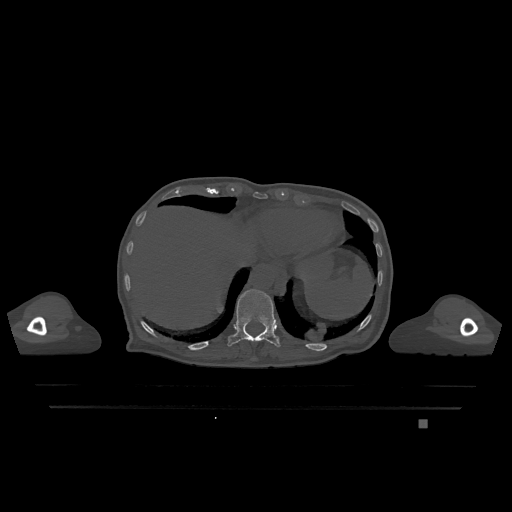
CT including the spine, one axial slice; slice 594 of 1317 in the series (ordered by position); bone window (W 1800 / L 400 HU); 0.5 mm slice thickness; 512 × 512 image matrix, field of view 500 × 500 mm. Patient: female, 74 years. From the clinical record (not read from this slice): primary cancer: lung; vertebrae with lytic lesions (as recorded): T1, T4, T5, T6, L4, L5.
Annotated regions visible in this slice (semi-automatic segmentation, software-assisted and operator-edited):
- T11 vertebra: box from (x=228, y=289) to (x=280, y=347) px